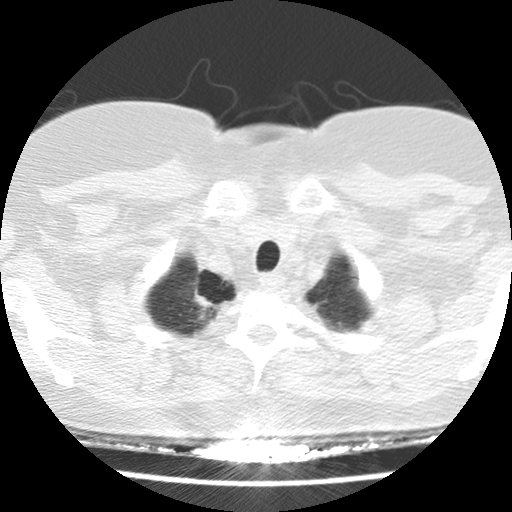
Low-dose screening chest CT, one axial slice; reconstruction kernel STANDARD; lung window (W 1500 / L -600 HU); 2.5 mm slice thickness; 512 × 512 image matrix, field of view 281 × 281 mm.
Annotated regions visible in this slice (outlined manually by an expert reader):
- lesion 1 (tumor, upper lobe of right lung): bounding box (x1, y1, x2, y2) in pixels: (194, 292, 217, 316)